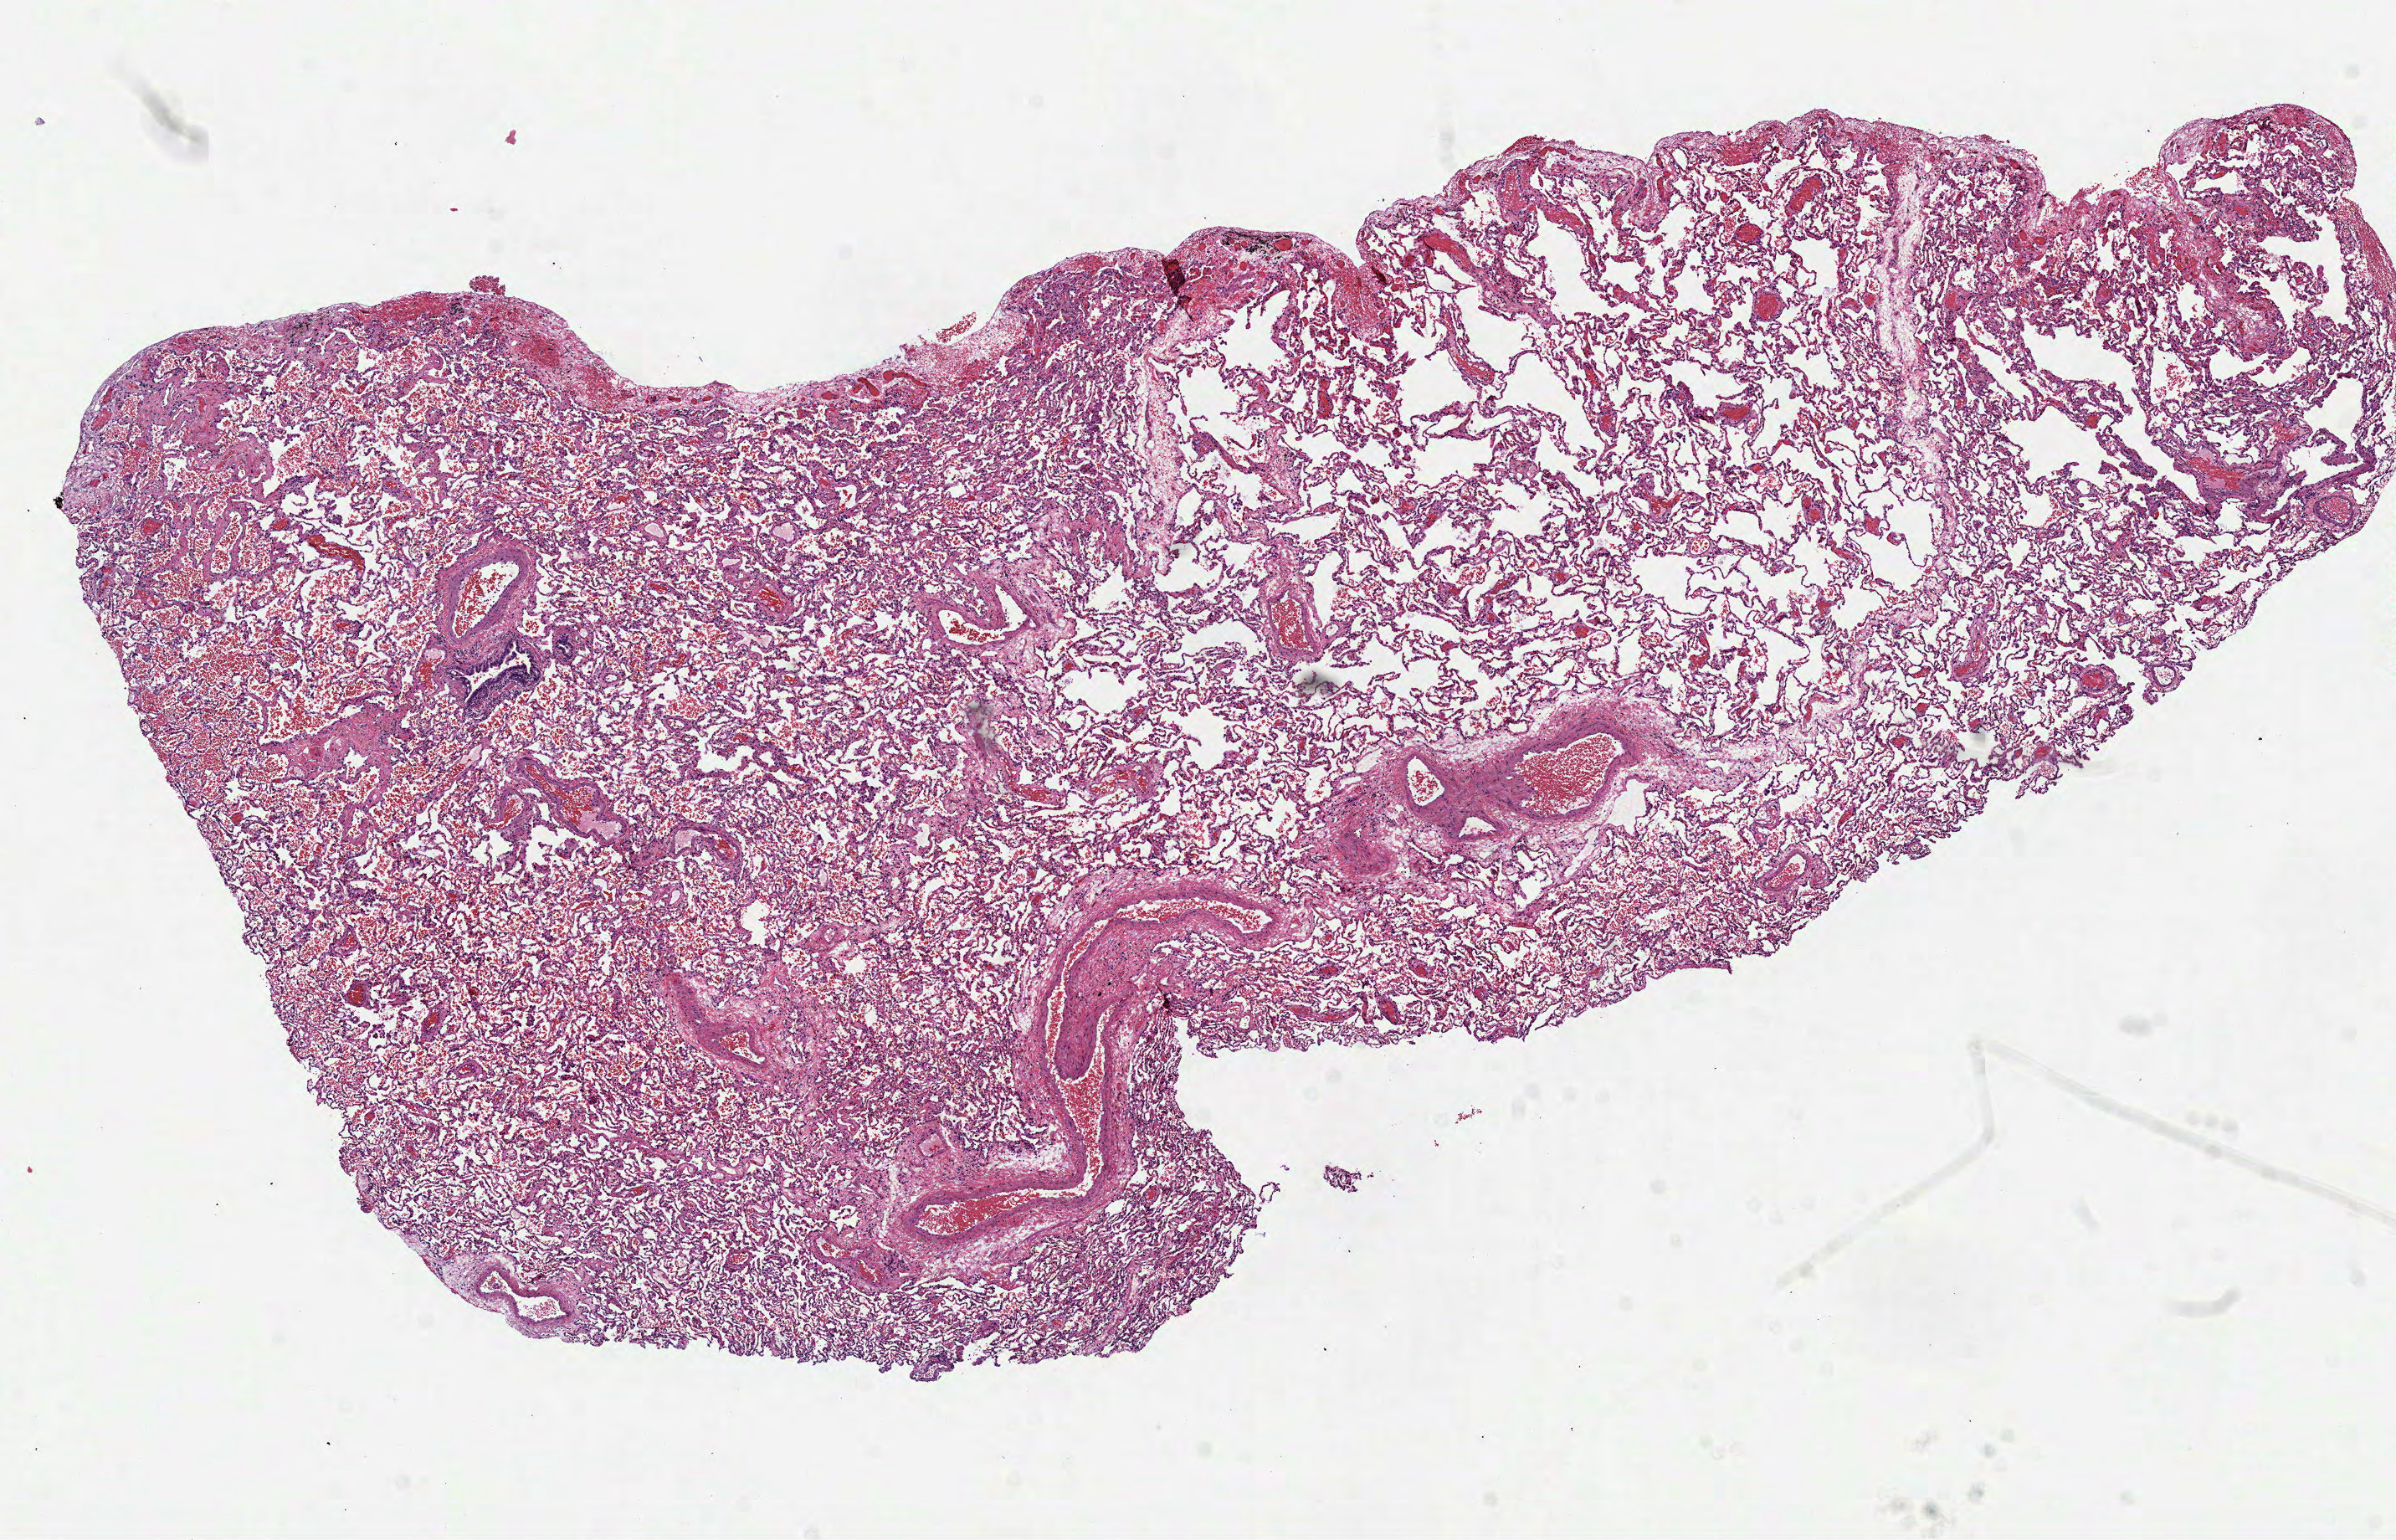
Whole-slide histology image, H&E — whole scanned area (about 11.5 x 7.4 mm, from a 40x scan) shown as a low-resolution overview; frozen section from the top of the tissue portion; solid tissue normal (non-tumour tissue) sample from the lung. Patient: female, age at initial diagnosis 67 years.
- this section: solid tissue normal (non-tumour) sample from the same patient
- patient diagnosis: Adenocarcinoma, NOS (upper lobe, lung)